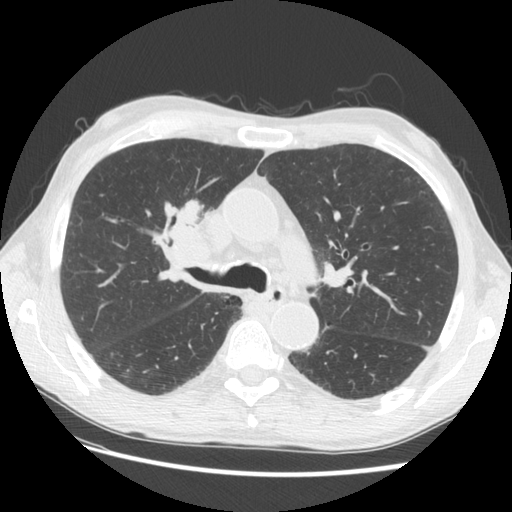
Chest CT (low-dose screening protocol), one axial image; third annual screen; lung window (W 1500 / L -600 HU); 2.5 mm slice thickness; standard (soft-tissue) reconstruction kernel (STANDARD). Male, age 73 years at enrolment. Current smoker at enrolment.
Lesion marked by an expert reader, bounding box [x1, y1, x2, y2] px = [141, 186, 235, 275]. The screening reader recorded 4 non-calcified nodules or masses ≥4 mm on this exam; which of them this box marks is not recorded. Later outcome: lung cancer diagnosed 48 days after this screen — squamous cell carcinoma, NOS, right upper lobe, poorly differentiated (G3), stage IIIB (AJCC 6th edition), 56 mm at pathology.